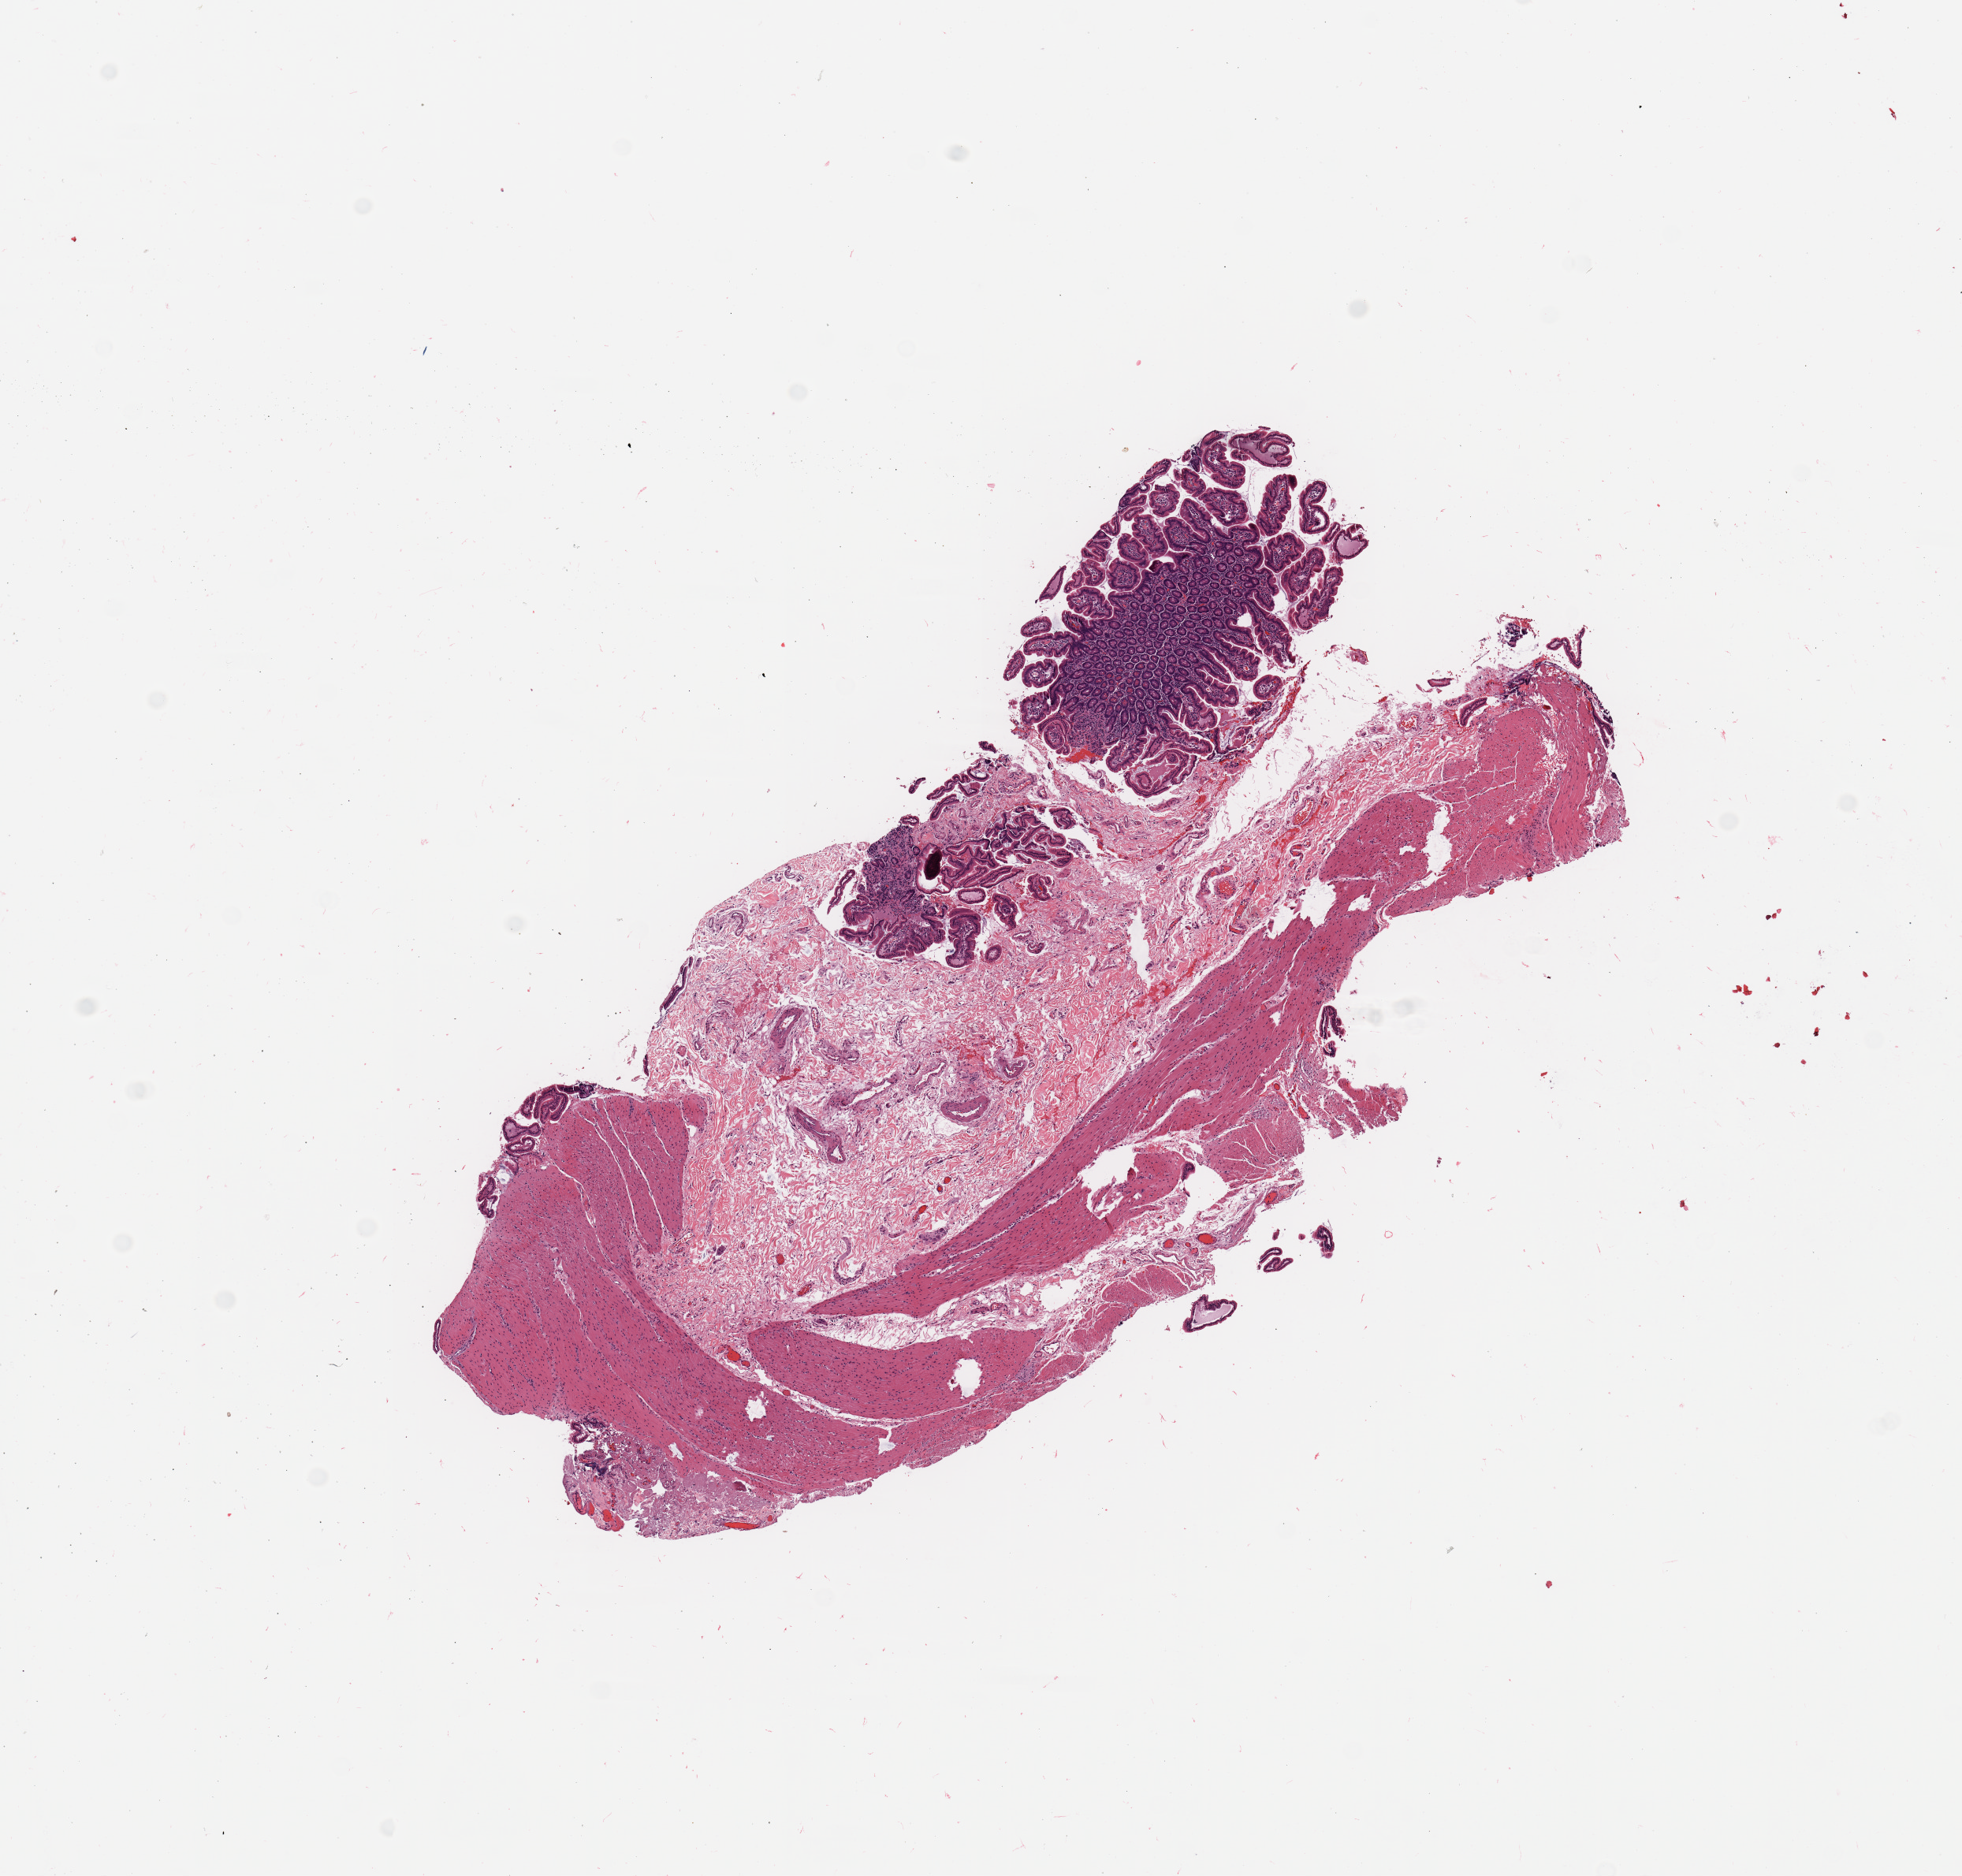
H&E whole-slide image — low-resolution overview of the scanned area, about 9.8 x 9.4 mm (acquisition: 20x scan); normal (non-tumour) tissue sample, pancreas. 63-year-old male patient.
* this section: normal (non-tumour) tissue from the same patient
* patient diagnosis: Infiltrating duct carcinoma, NOS